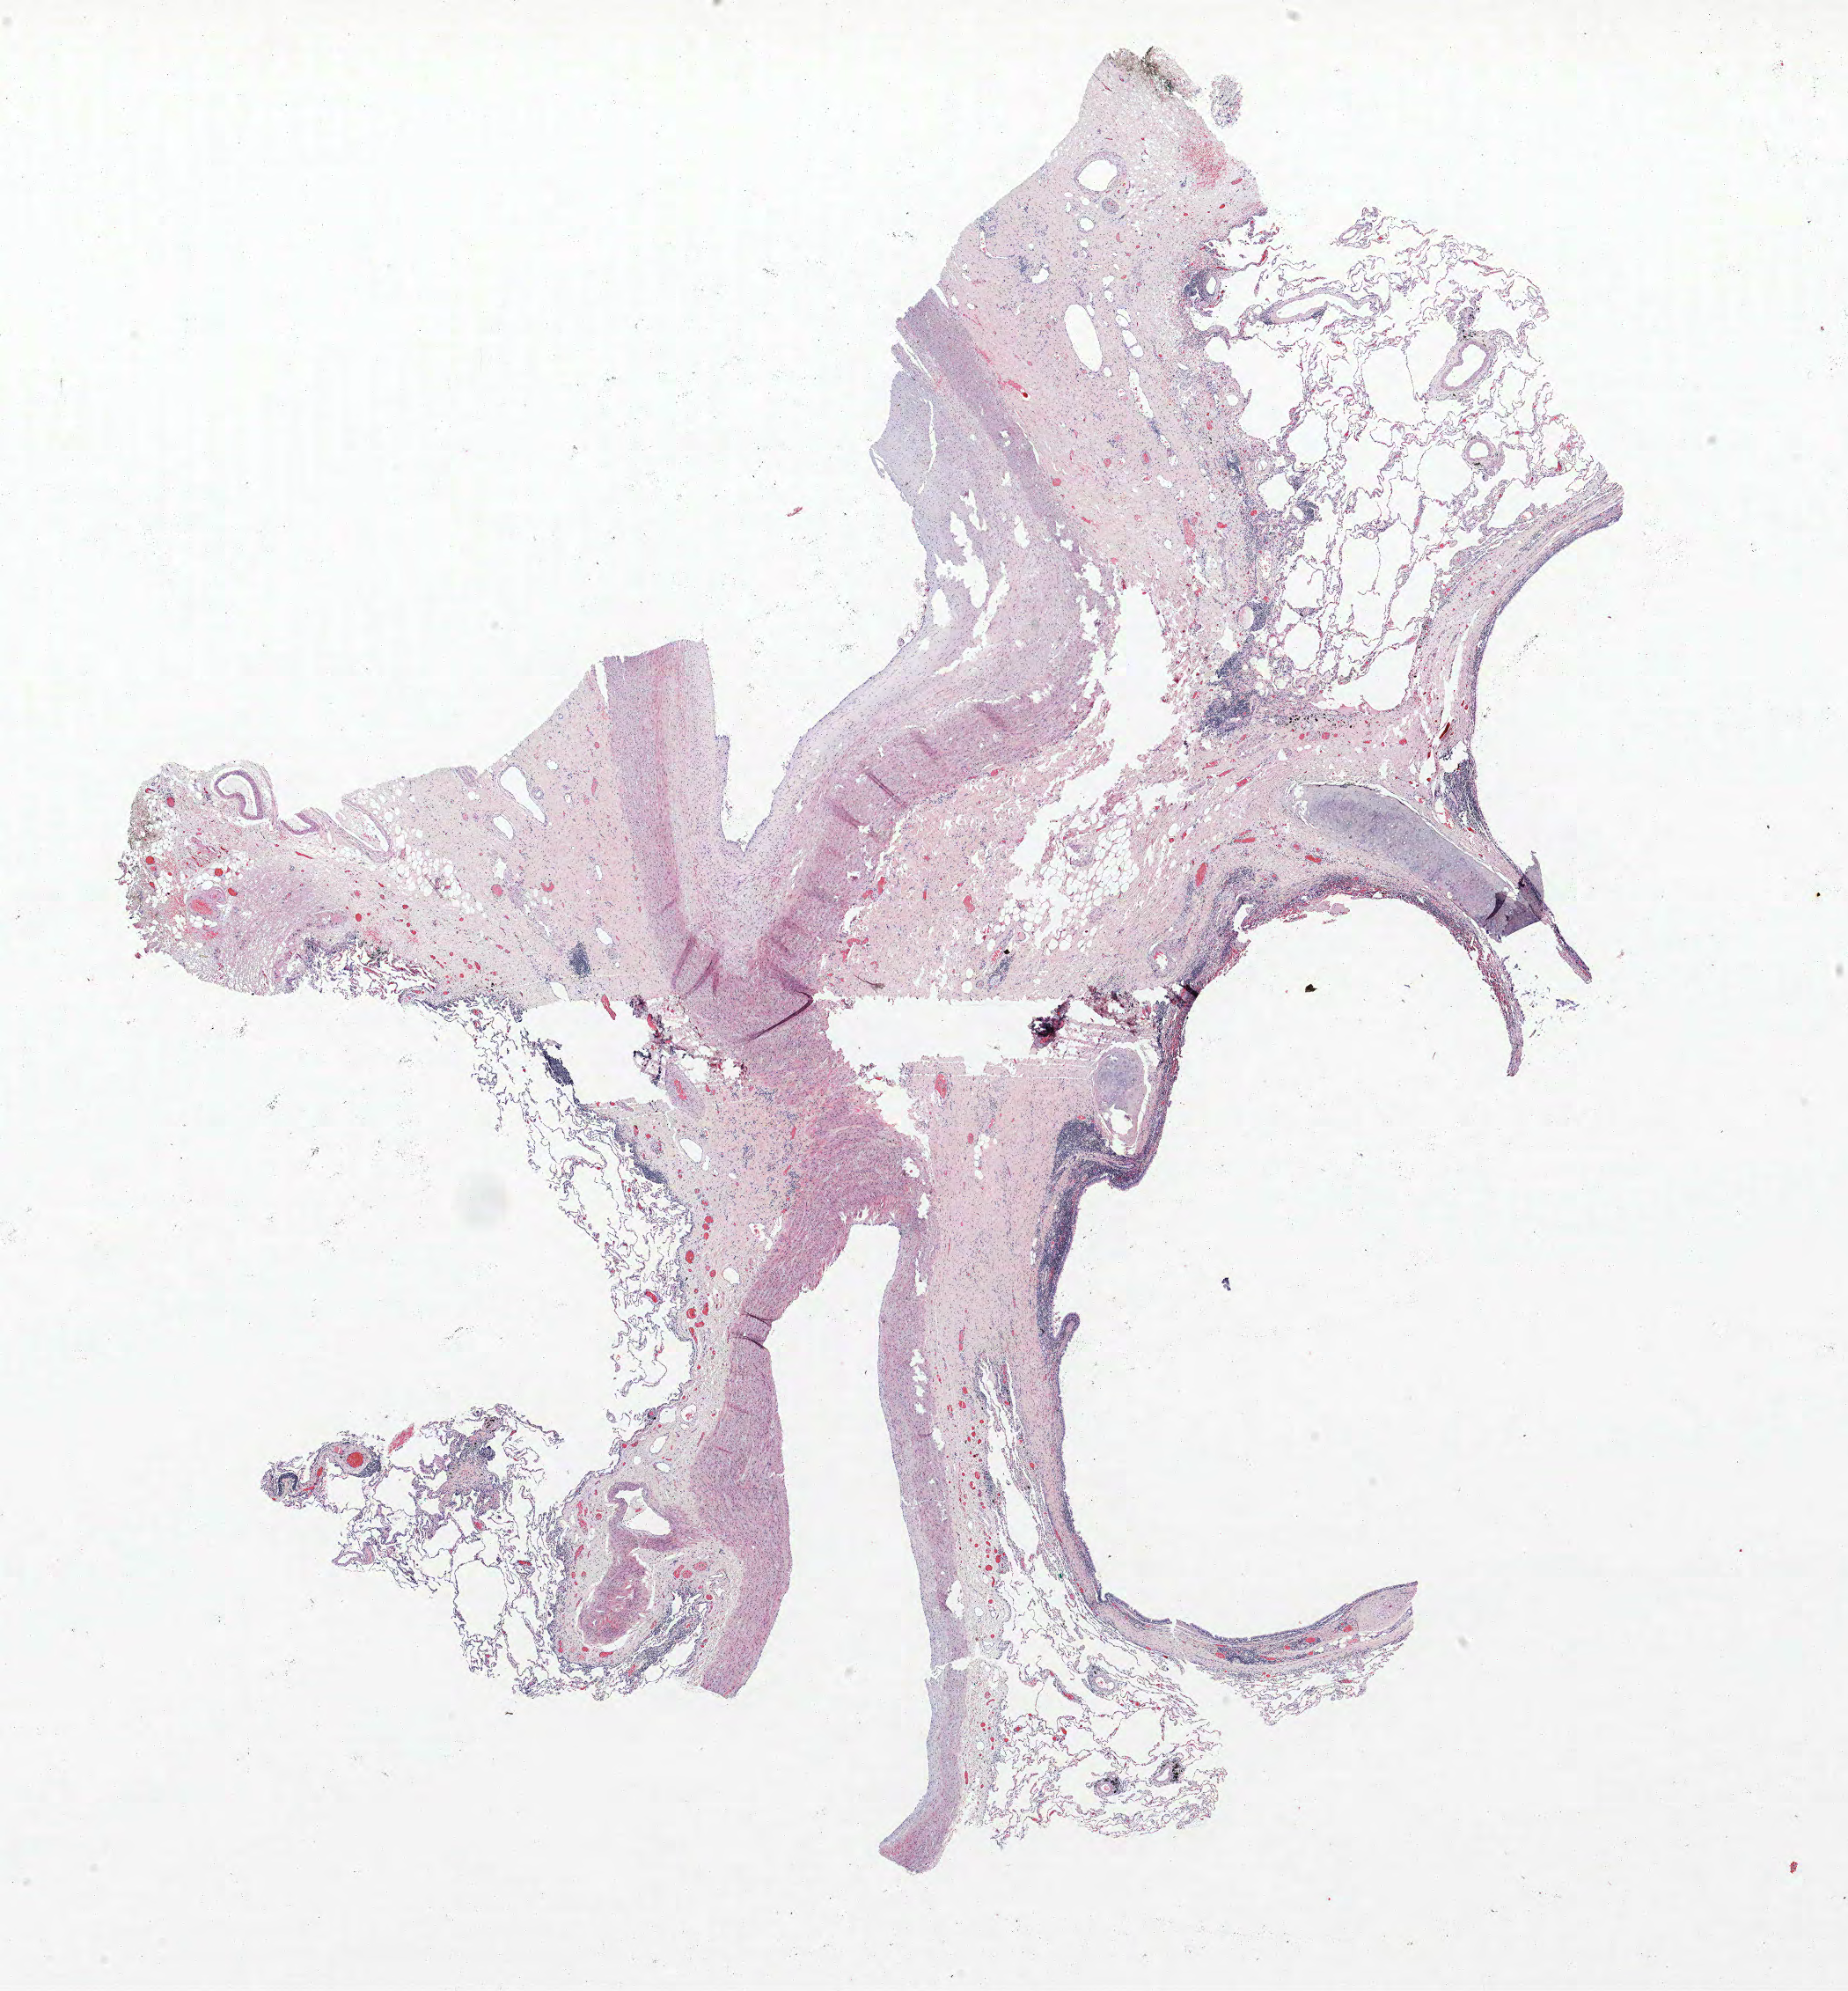
H&E whole-slide image — low-resolution overview of the scanned area, about 16.8 x 18.1 mm (from a 40x scan); formalin-fixed paraffin-embedded (FFPE) section; lung. Male, age 68 at enrolment. Former smoker at enrolment.
Participant's lung-cancer diagnosis: Squamous cell carcinoma, NOS (ICD-O-3 8070/3).